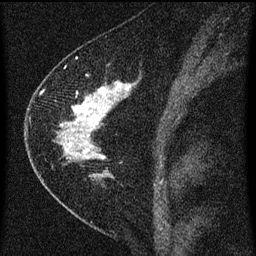
Breast MRI (dynamic contrast-enhanced), one sagittal slice. Slice 34 of 60 in the series (ordered by position). Dynamic contrast-enhanced series, image 2 of 3 at this slice position (ordered by acquisition). 1.5 T. TE 4.2 ms, TR 8 ms. 2 mm slice thickness. 256 × 256 image matrix, field of view 180 × 180 mm. Patient: female, 47 years.
Outlined on this slice (semi-automatic segmentation, software-assisted and operator-edited):
- analysis volume of interest (the breast-tissue region the enhancement analysis was run in; not a lesion): box from (x=38, y=76) to (x=137, y=193) px
- tumour enhancement mask (voxels above the 70 % enhancement threshold inside the analysis volume of interest): (x=59, y=84)–(x=129, y=177)